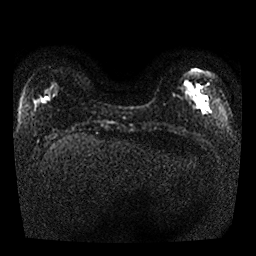
Breast MRI, one axial slice; position 6 of 25 along the scan axis; diffusion-weighted series; image 2 of 4 stored at this slice position (different b-values; order by instance number); 1.5 T; 256 × 256 image matrix. Female patient.
Annotated regions visible in this slice (outlined manually by an expert reader):
- tumour on diffusion-weighted imaging: box from (x=187, y=86) to (x=197, y=98) px